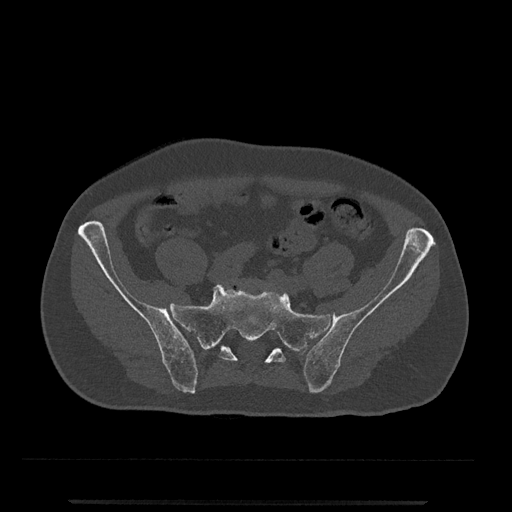
CT including the spine, one axial slice. Slice 10 of 797 in the series (ordered by position). 120 kVp. Bone window (W 1800 / L 400 HU). 0.5 mm slice thickness. 512 × 512 image matrix, field of view 419 × 419 mm. Male patient, age 63 years. Case-level facts recorded for this patient, not image findings: primary cancer: prostate.
Structures marked on this image (semi-automatic segmentation, software-assisted and operator-edited):
- L5 vertebra: bounding box [x1, y1, x2, y2] px = [231, 279, 237, 282]